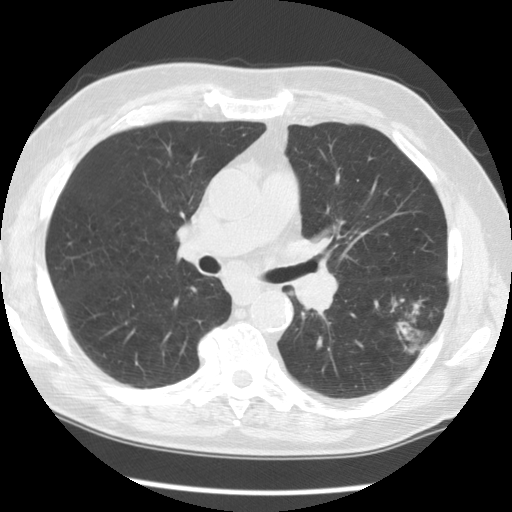
Low-dose screening chest CT, one axial slice; position 79 of 130 along the scan axis; reconstruction kernel STANDARD; 120 kVp; lung window (W 1500 / L -600 HU); 2.5 mm slice thickness; 512 × 512 image matrix.
Outlined on this slice (expert manual segmentation):
- lesion 1 (tumor, lower lobe of left lung): box from (x=397, y=299) to (x=432, y=353) px